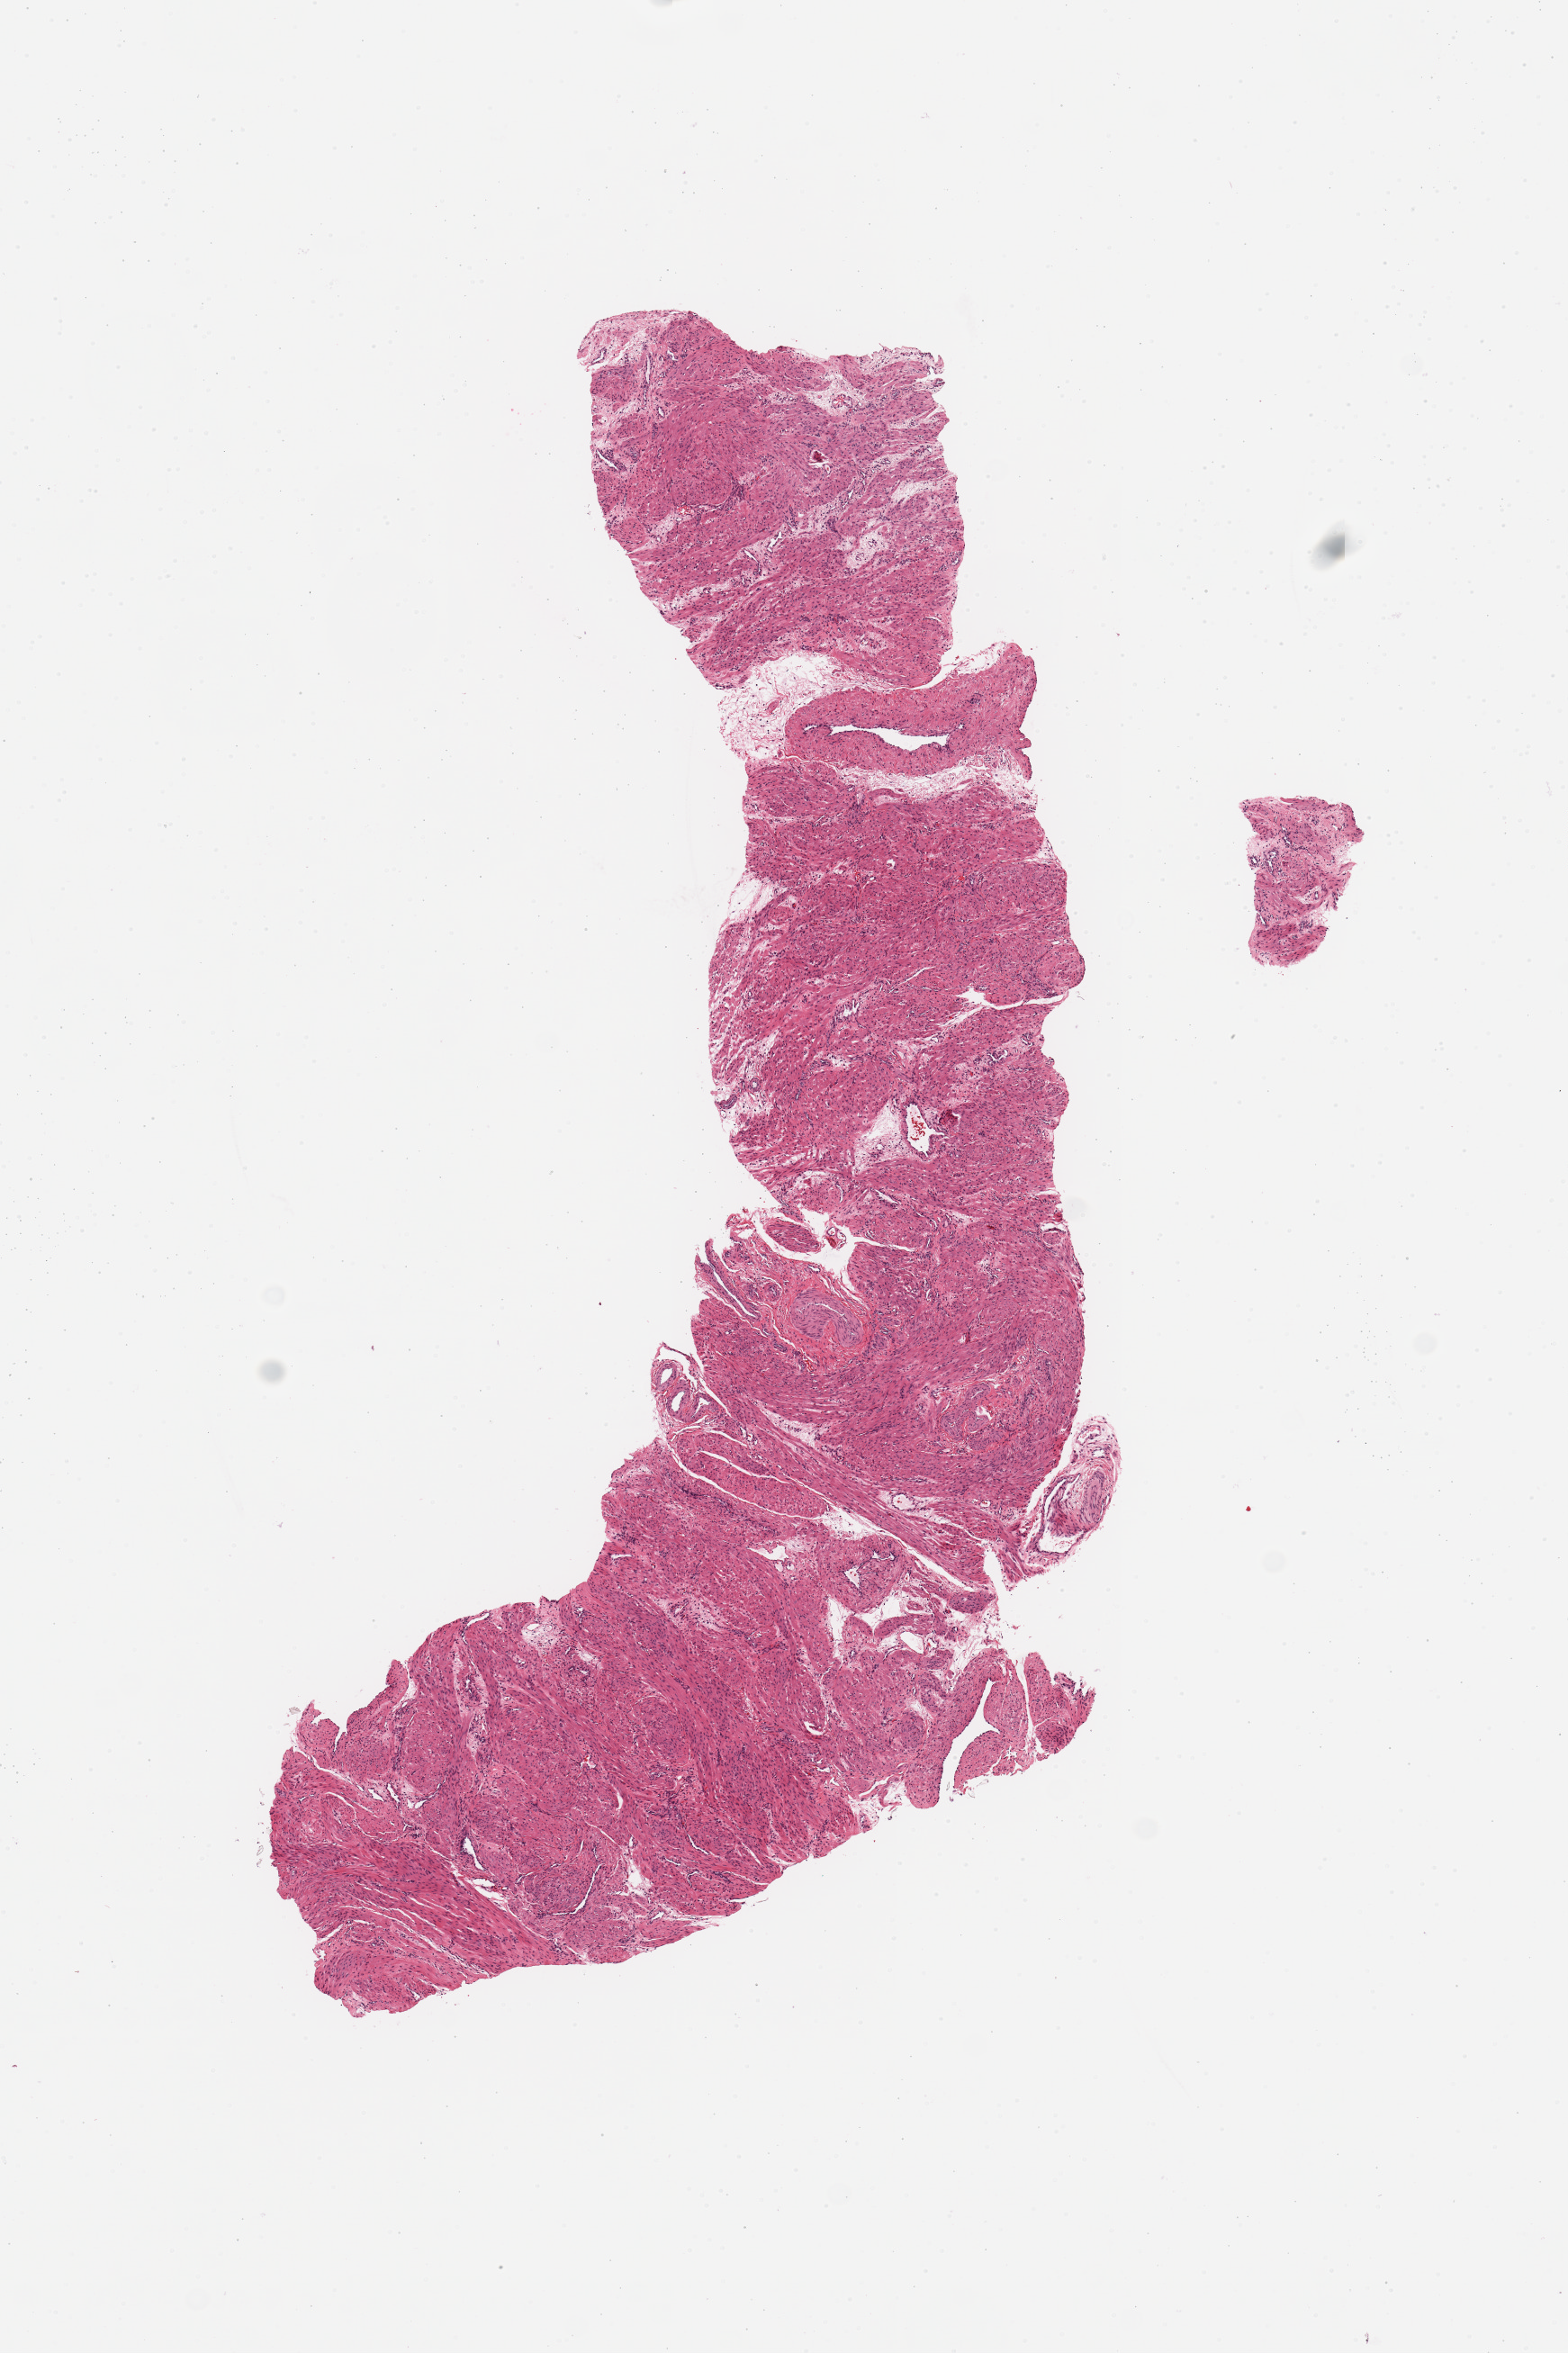
Whole-slide histology image, H&E-stained, whole scanned area (about 6.9 x 10.3 mm) shown as a low-resolution overview; uterus, normal (non-tumour) tissue. Female, 49 y/o.
This section: normal (non-tumour) tissue from the same patient. Patient diagnosis (cohort enrolment): corpus endometrial carcinoma (uterus).